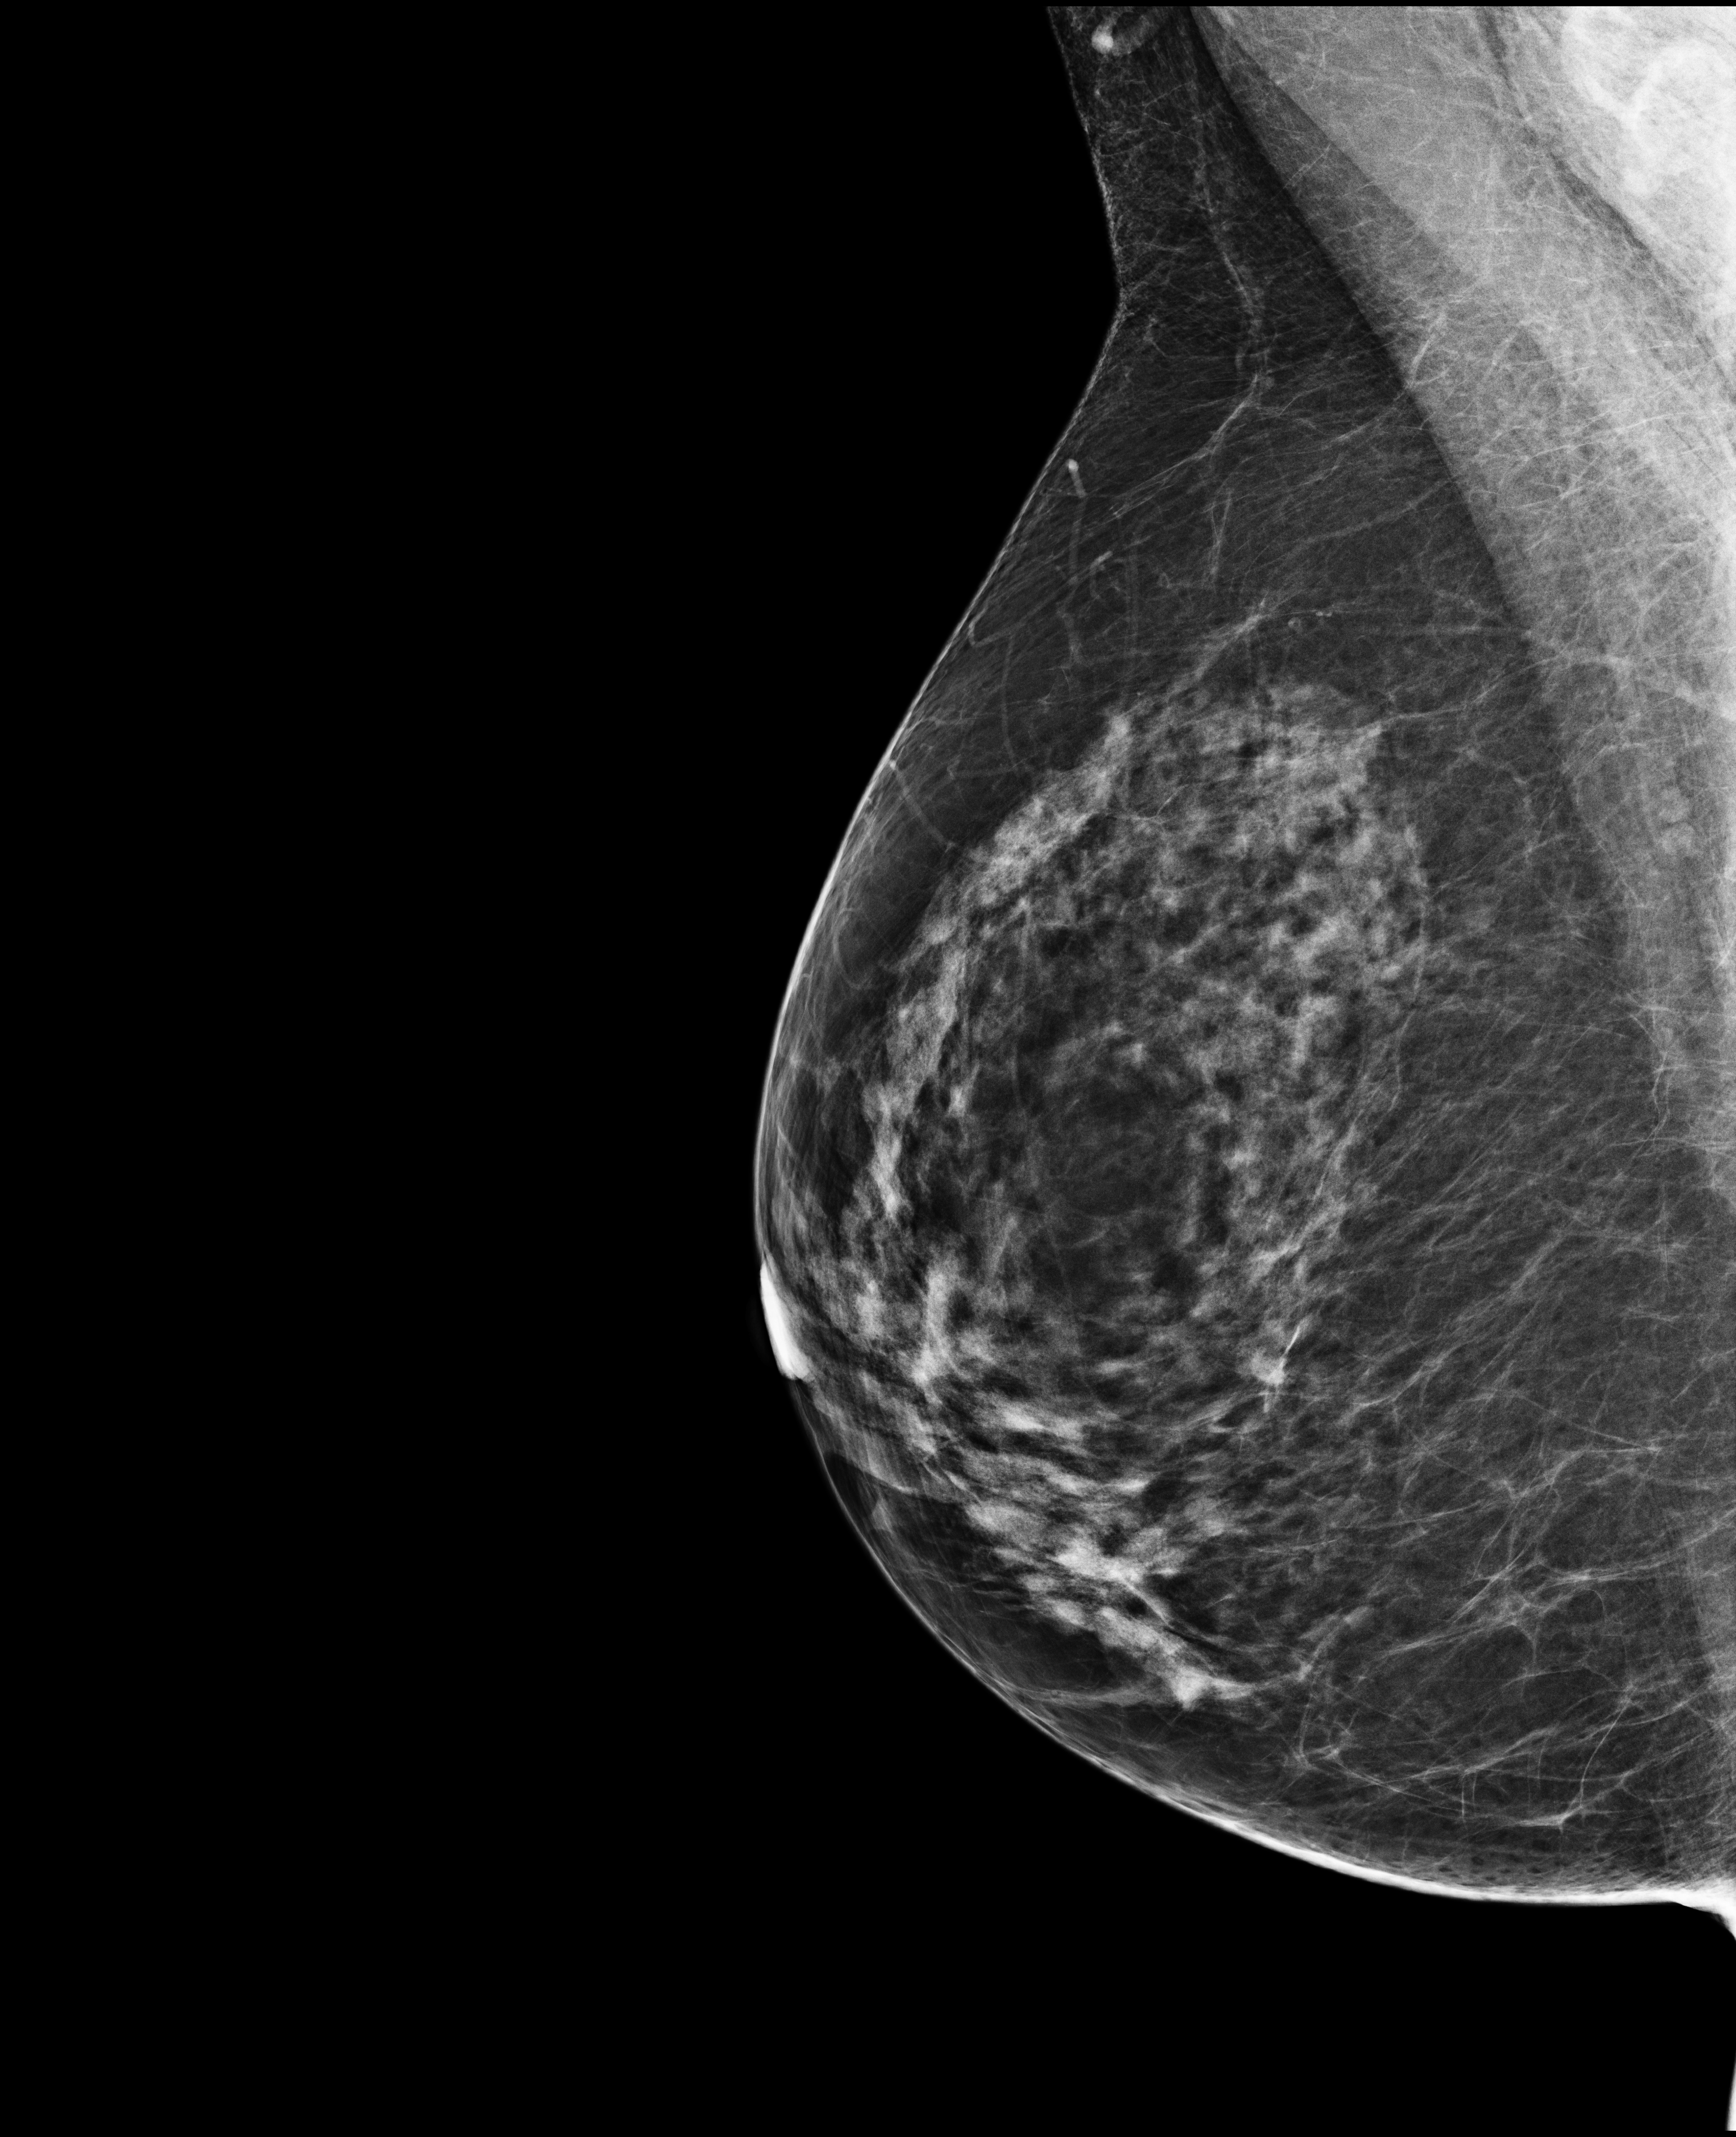
Full-field digital mammogram (FFDM); right breast; mediolateral oblique (MLO) view; screening examination. Female patient, age 52 years.
BI-RADS breast density category at the screening exam (both breasts, scale 1–4): 3. Final BI-RADS assessment for this screening round (tomosynthesis exam, both breasts): category 1. Recall: no recall after this screen.